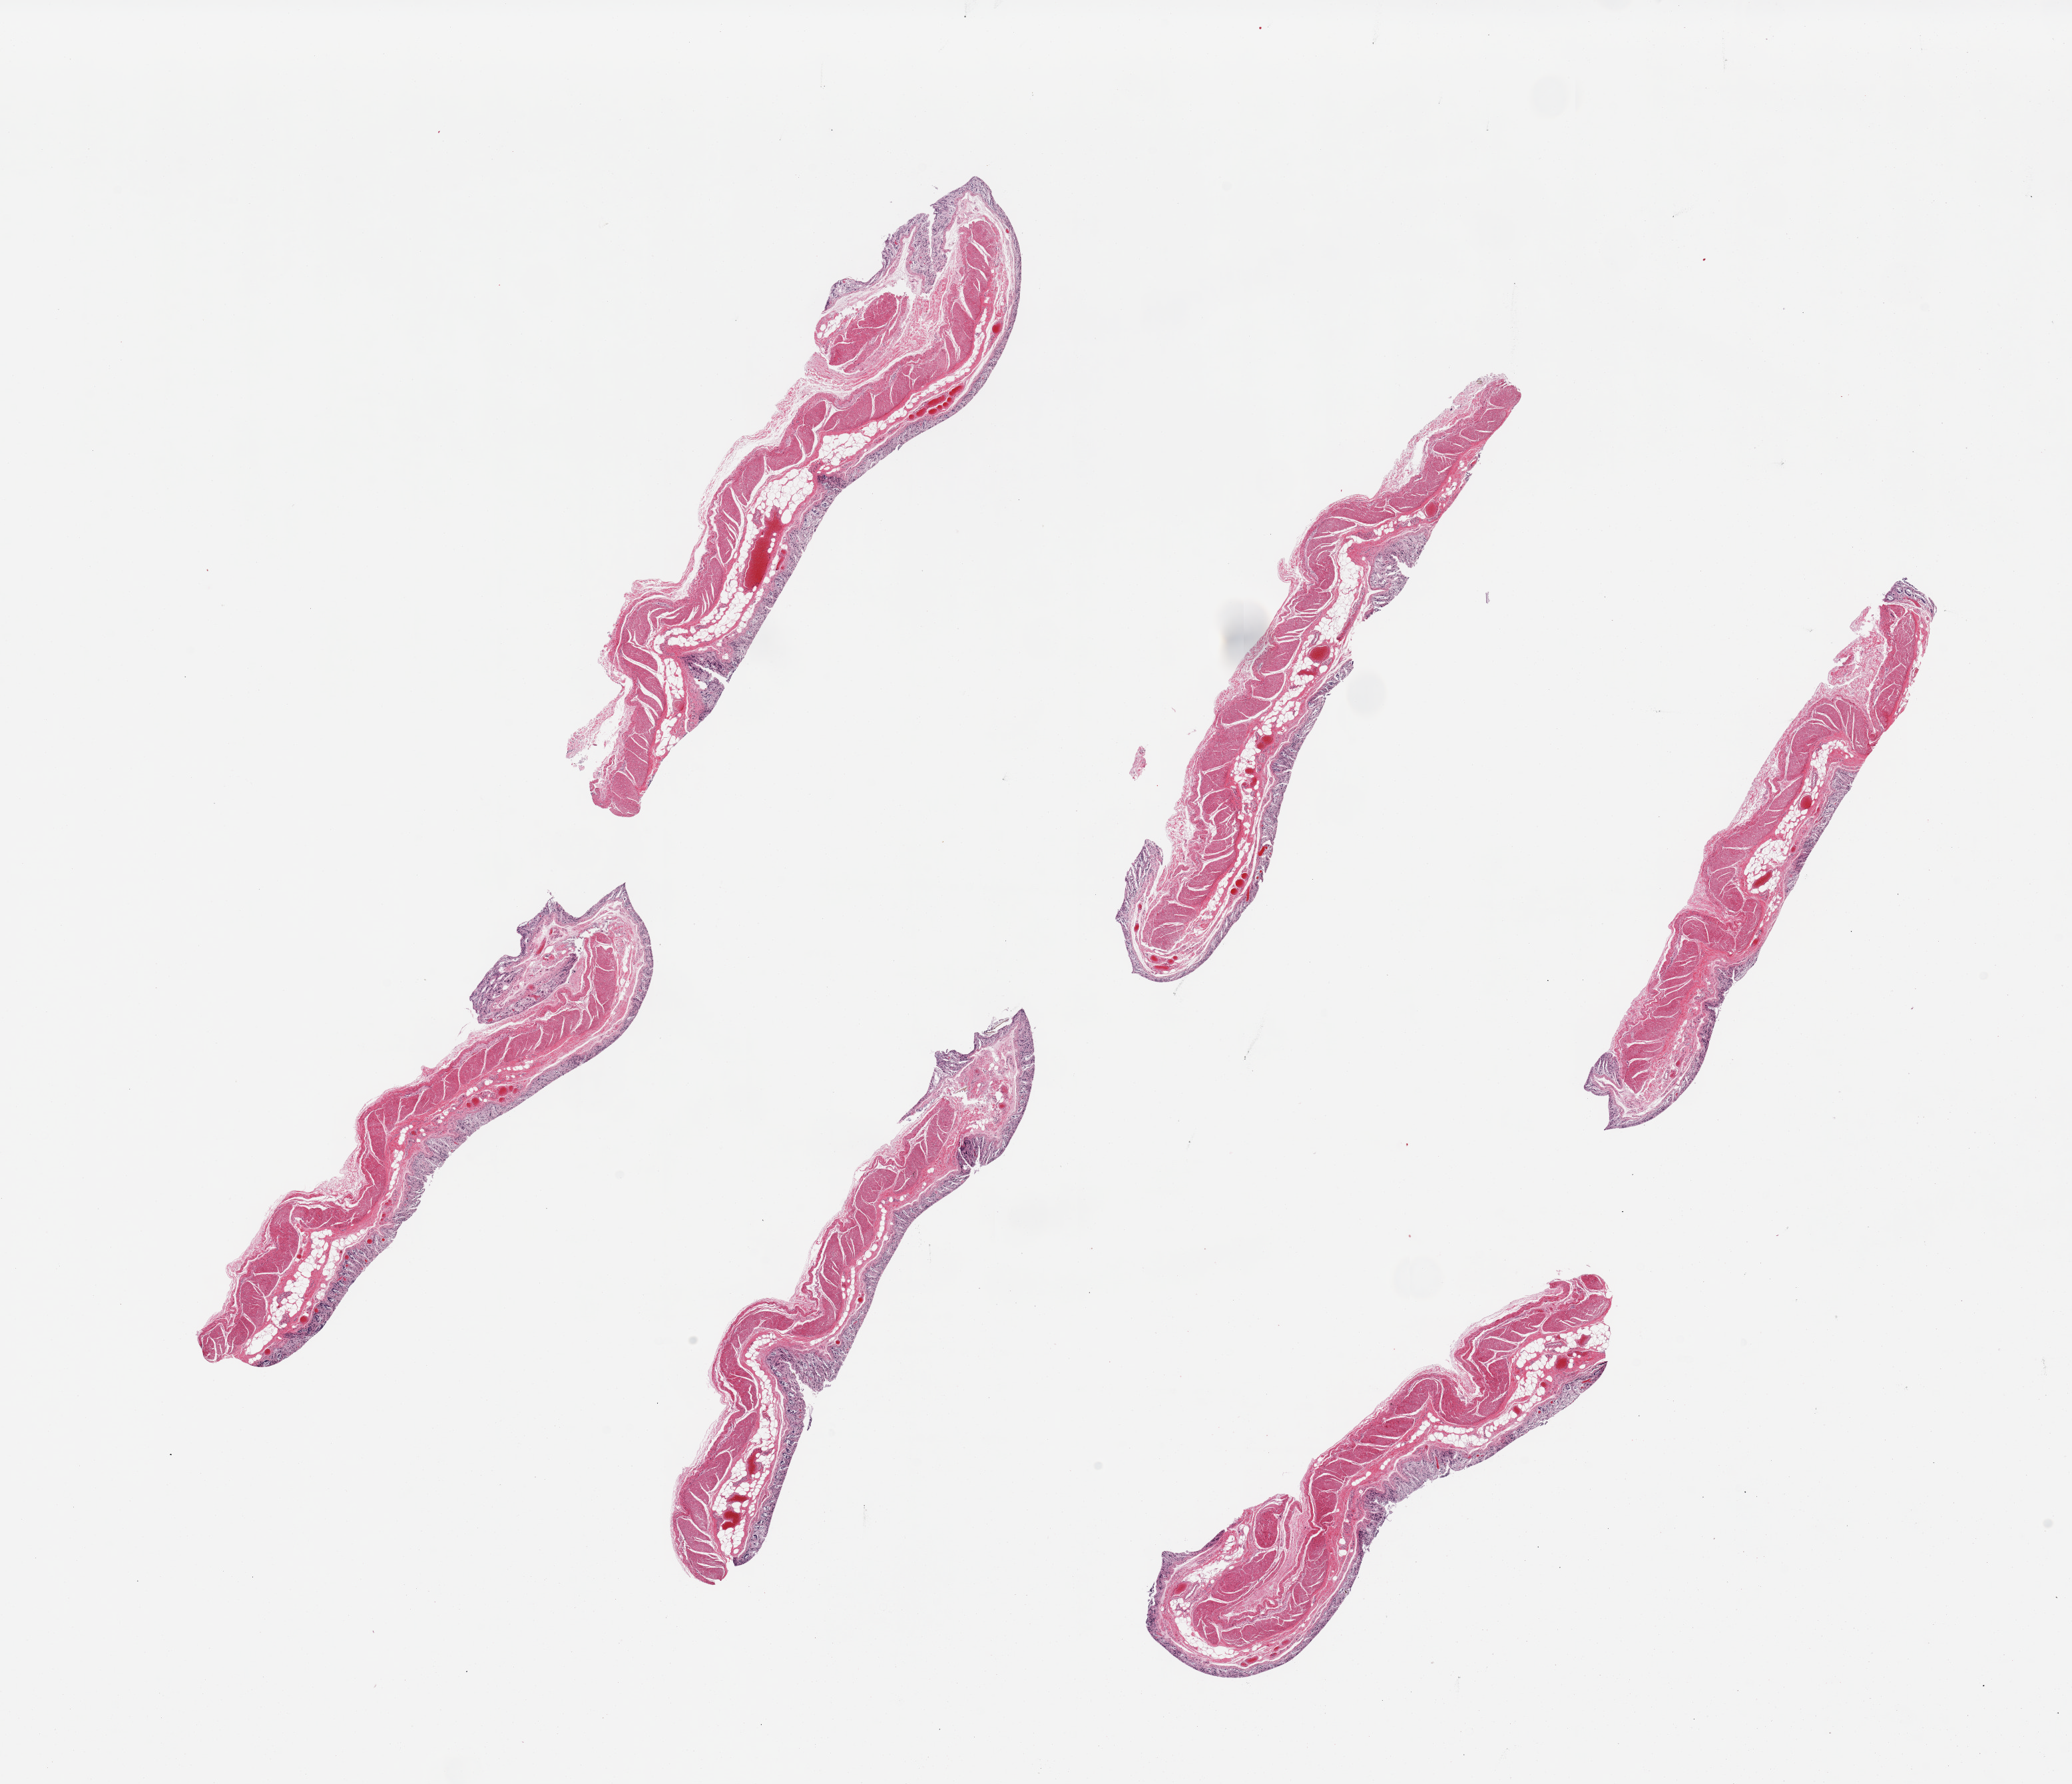
Whole-slide image, H&E stain, brightfield, whole scanned area (about 24.6 x 21.2 mm) shown as a low-resolution overview. PAXgene-fixed, paraffin-embedded tissue. Section of transverse colon (target tissue). Tissue donor sample. Male donor.
Pathologist's review note for this sample: 6 pieces. Mucosa totally autolyzed; muscle slightly autolyzed.